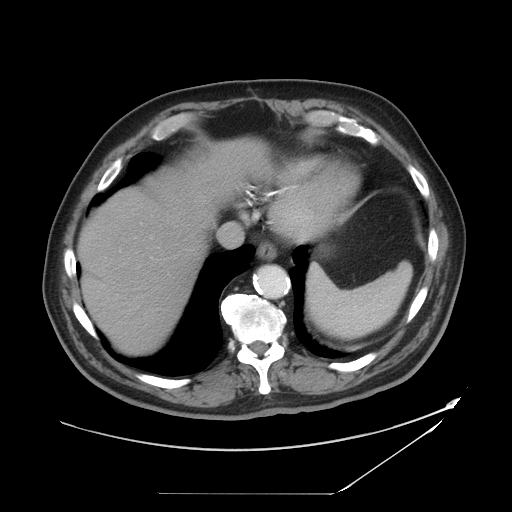
Contrast-enhanced abdominal CT, one axial slice. Position 39 of 49 along the scan axis. 120 kVp. Soft-tissue window (W 400 / L 40 HU). 5 mm slice thickness. 512 × 512 image matrix, field of view 461 × 461 mm. Male patient, age 72 years. From the clinical record (not read from this slice): diagnosis: colorectal cancer liver metastases, imaged before liver resection; multiple liver metastases: no; largest metastasis: 2.5 cm; disease in both lobes: no.
Structures marked on this image (outlined manually by an expert reader):
- liver: box from (x=81, y=144) to (x=260, y=353) px
- planned liver remnant (the part of the liver to remain after resection): (x=80, y=191)–(x=204, y=353)